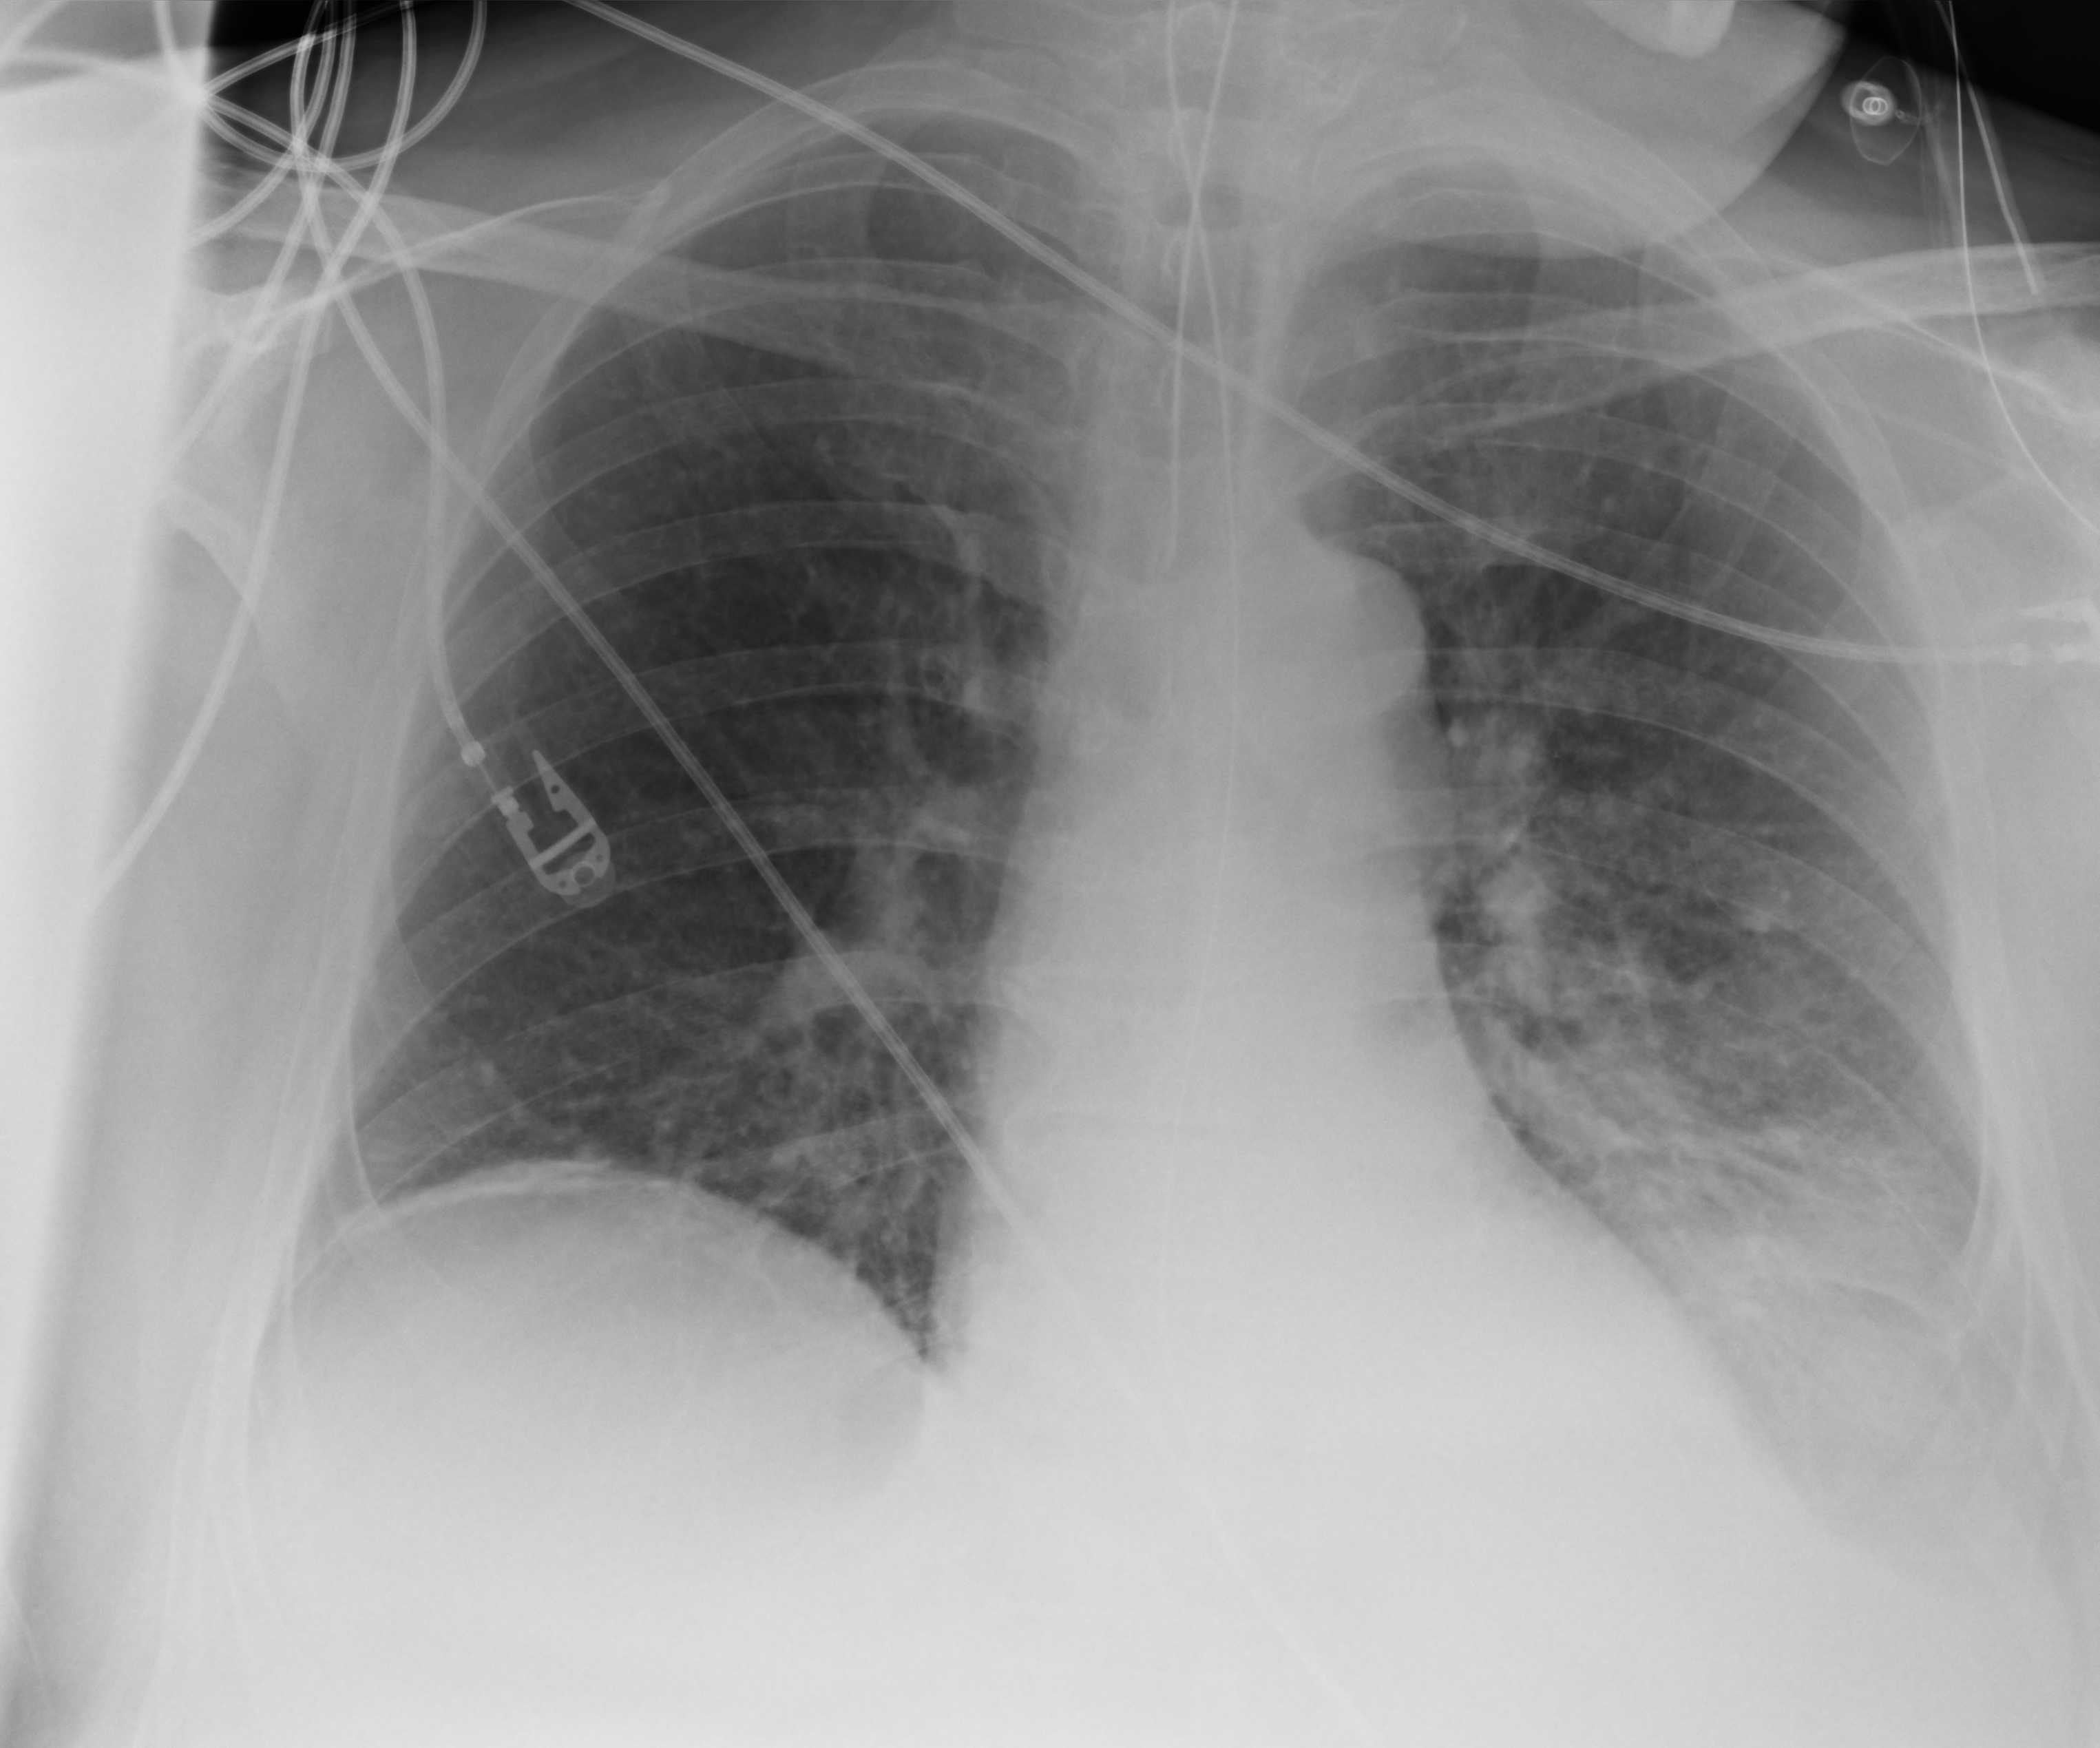
Portable chest radiograph; anteroposterior (AP) projection. Male patient hospitalised with COVID-19, age 60–74 years.
Admission-level facts for this patient (not findings on this image; timing relative to this image not recorded):
- length of hospital stay: 22 days
- mechanically ventilated during this hospital stay: yes